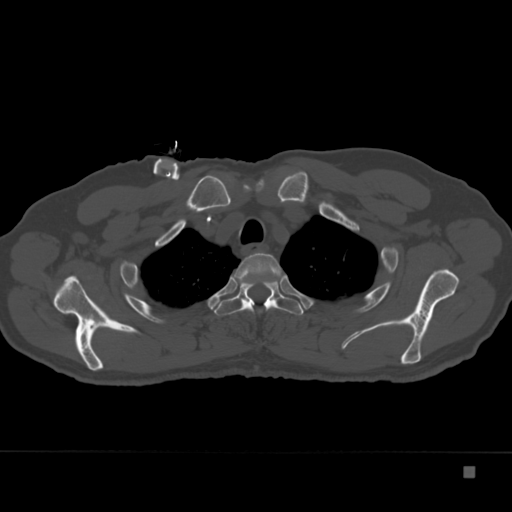
CT including the spine, one axial slice; slice 291 of 332 in the series (ordered by position); reconstruction kernel Br40s; 120 kVp; bone window (W 1800 / L 400 HU); 1.5 mm slice thickness; 512 × 512 image matrix, field of view 389 × 389 mm. Patient: male, 72 years. Case-level facts recorded for this patient, not image findings: primary cancer: skeletal.
Structures marked on this image (semi-automatically segmented with operator editing):
- T2 vertebra: bounding box <230,253,281,286> (left, top, right, bottom; pixels)
- T3 vertebra: <214,277,304,316>